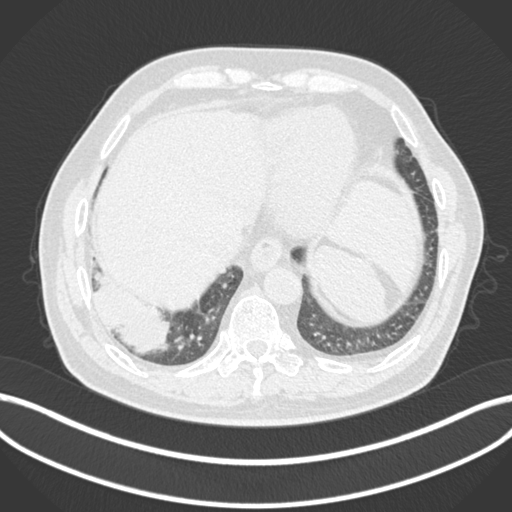
Chest CT, one axial slice; position 24 of 200 along the scan axis; 120 kVp; lung window (W 1500 / L -600 HU); 1 mm slice thickness; 512 × 512 image matrix. Patient: male, 59 years.
Outlined on this slice (rectangle marked by the reading radiologist):
- lung tumour (recorded histology: adenocarcinoma): bounding box [x1, y1, x2, y2] px = [85, 270, 171, 356]